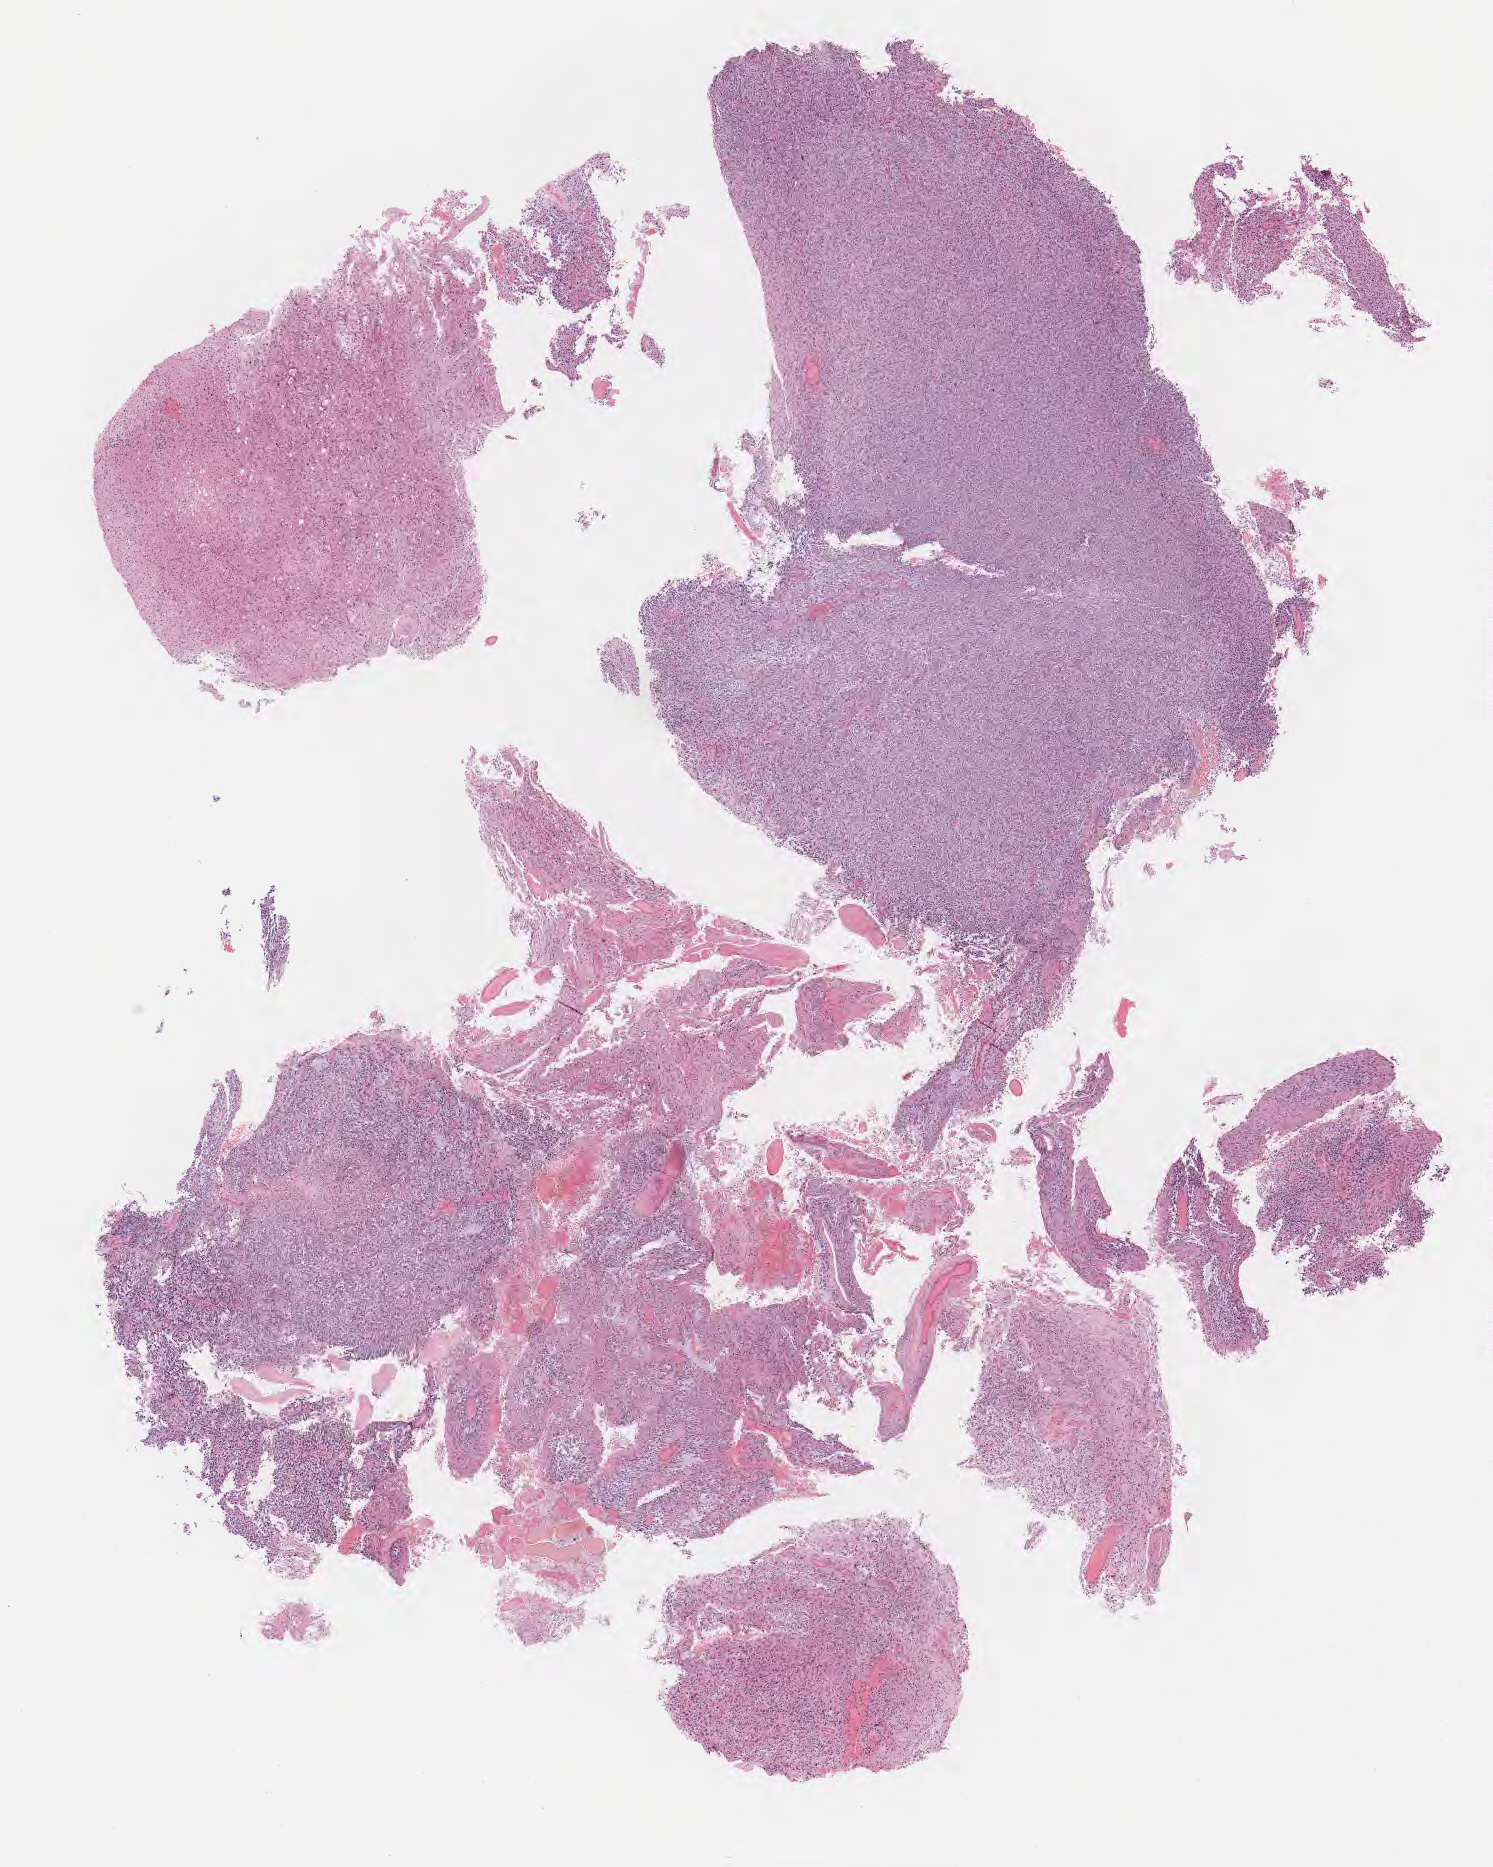
H&E whole-slide image — a low-resolution overview of the entire scanned area, about 12.1 x 15.1 mm, formalin-fixed, paraffin-embedded (FFPE) tissue, specimen: primary tumor, site: brain. Male, age 69 years at initial diagnosis. Slide review estimates, as recorded: tumor cells 84%, tumor nuclei 91%, stromal cells 6%, necrosis 2%, normal cells 8%. Inflammatory infiltration, as recorded: lymphocyte infiltration 0%, monocyte infiltration 0%, neutrophil infiltration 0%.
Histologic diagnosis: Glioblastoma, NOS. Section: bottom of the tissue portion.